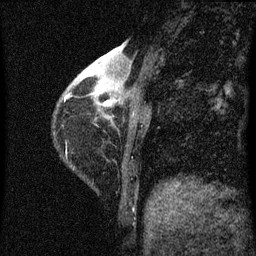
Breast MRI (dynamic contrast-enhanced), one sagittal slice. Position 14 of 60 along the scan axis. Dynamic contrast-enhanced series, image 2 of 3 at this slice position (ordered by acquisition). 1.5 T. TE 4.2 ms, TR 8 ms. 2 mm slice thickness. 256 × 256 image matrix, field of view 180 × 180 mm. Patient: female, 38 years.
Outlined on this slice (semi-automatically segmented with operator editing):
- analysis volume of interest (the breast-tissue region the enhancement analysis was run in; not a lesion): bounding box (x1, y1, x2, y2) in pixels: (67, 44, 144, 127)
- tumour enhancement mask (voxels above the 70 % enhancement threshold inside the analysis volume of interest): (100, 58, 112, 107)